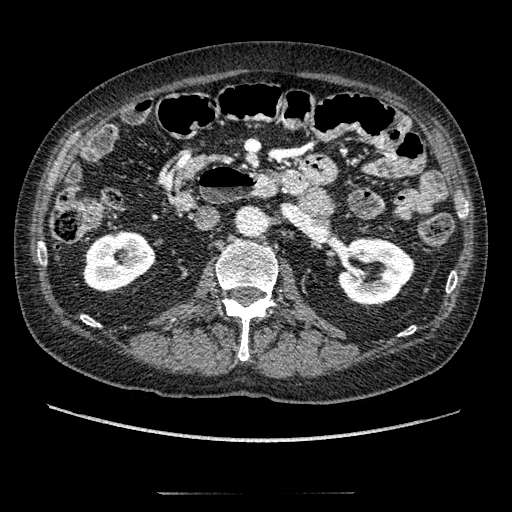
Contrast-enhanced abdominal CT, one axial slice; slice 81 of 274 in the series (ordered by position); reconstruction kernel STANDARD; intravenous contrast given; soft-tissue window (W 400 / L 40 HU); 512 × 512 image matrix. Male patient, age 69 years. From the clinical record (not read from this slice): diagnosis: adrenocortical carcinoma; tumour side: left adrenal; tumour size at pathology: 6.1 cm; Ki-67 index: 10 %; stage (as recorded): 3.
Structures marked on this image (semi-automatic segmentation, software-assisted and operator-edited):
- mass: bounding box (x1, y1, x2, y2) in pixels: (302, 188, 333, 217)